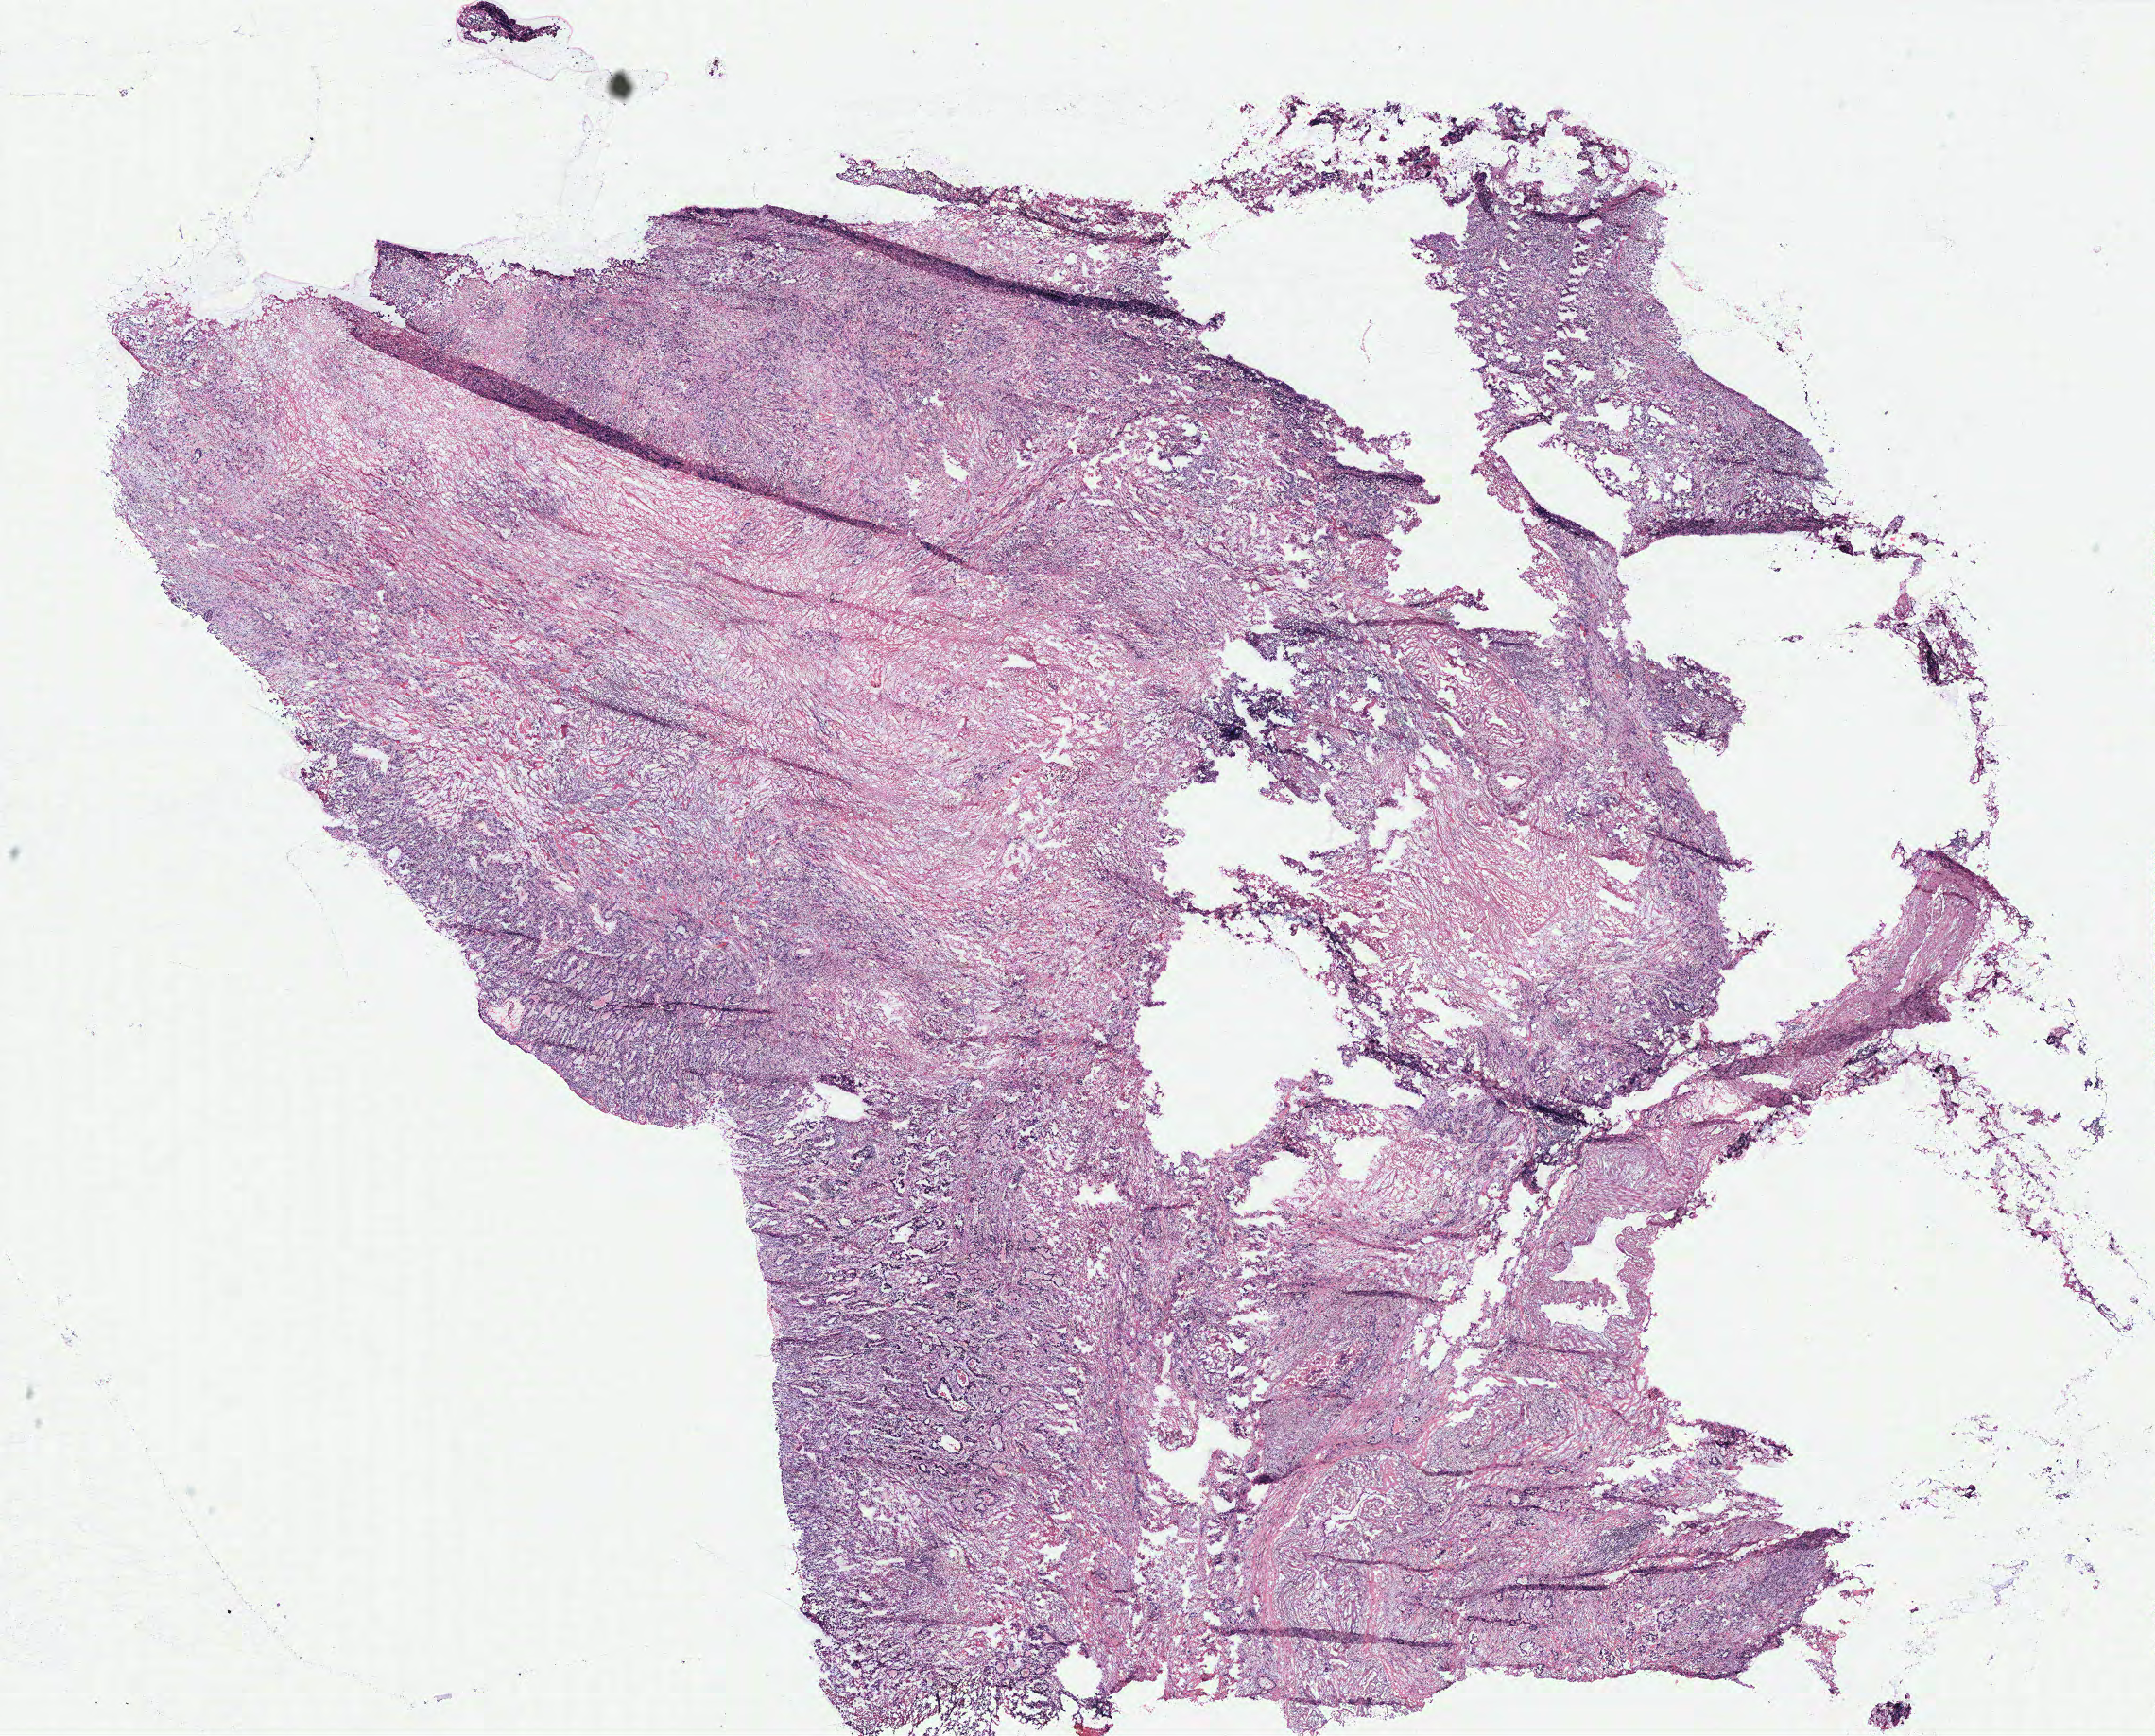
Whole-slide histology image, H&E — shown as a low-resolution overview of the whole scanned area (about 18.2 x 14.7 mm). Colon, tissue type not recorded.
Patient diagnosis (cohort enrolment): colon cancer (colon).